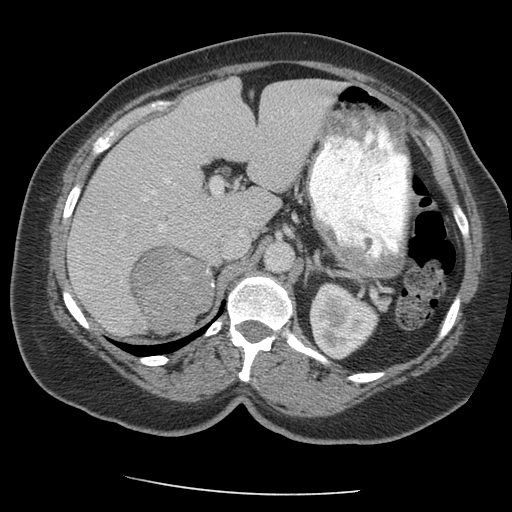
Contrast-enhanced abdominal CT, one axial slice. Slice 127 of 163 in the series (ordered by position). Reconstruction kernel STANDARD. 140 kVp. Intravenous contrast given. Soft-tissue window (W 400 / L 40 HU). 512 × 512 image matrix. Patient: female, 70 years. From the clinical record (not read from this slice): diagnosis: adrenocortical carcinoma; tumour side: right adrenal; tumour size at pathology: 9.5 cm; Ki-67 index: 5 %; stage (as recorded): 2.
Annotated regions visible in this slice (semi-automatic segmentation, software-assisted and operator-edited):
- mass: bounding box (x1, y1, x2, y2) in pixels: (133, 249, 210, 335)